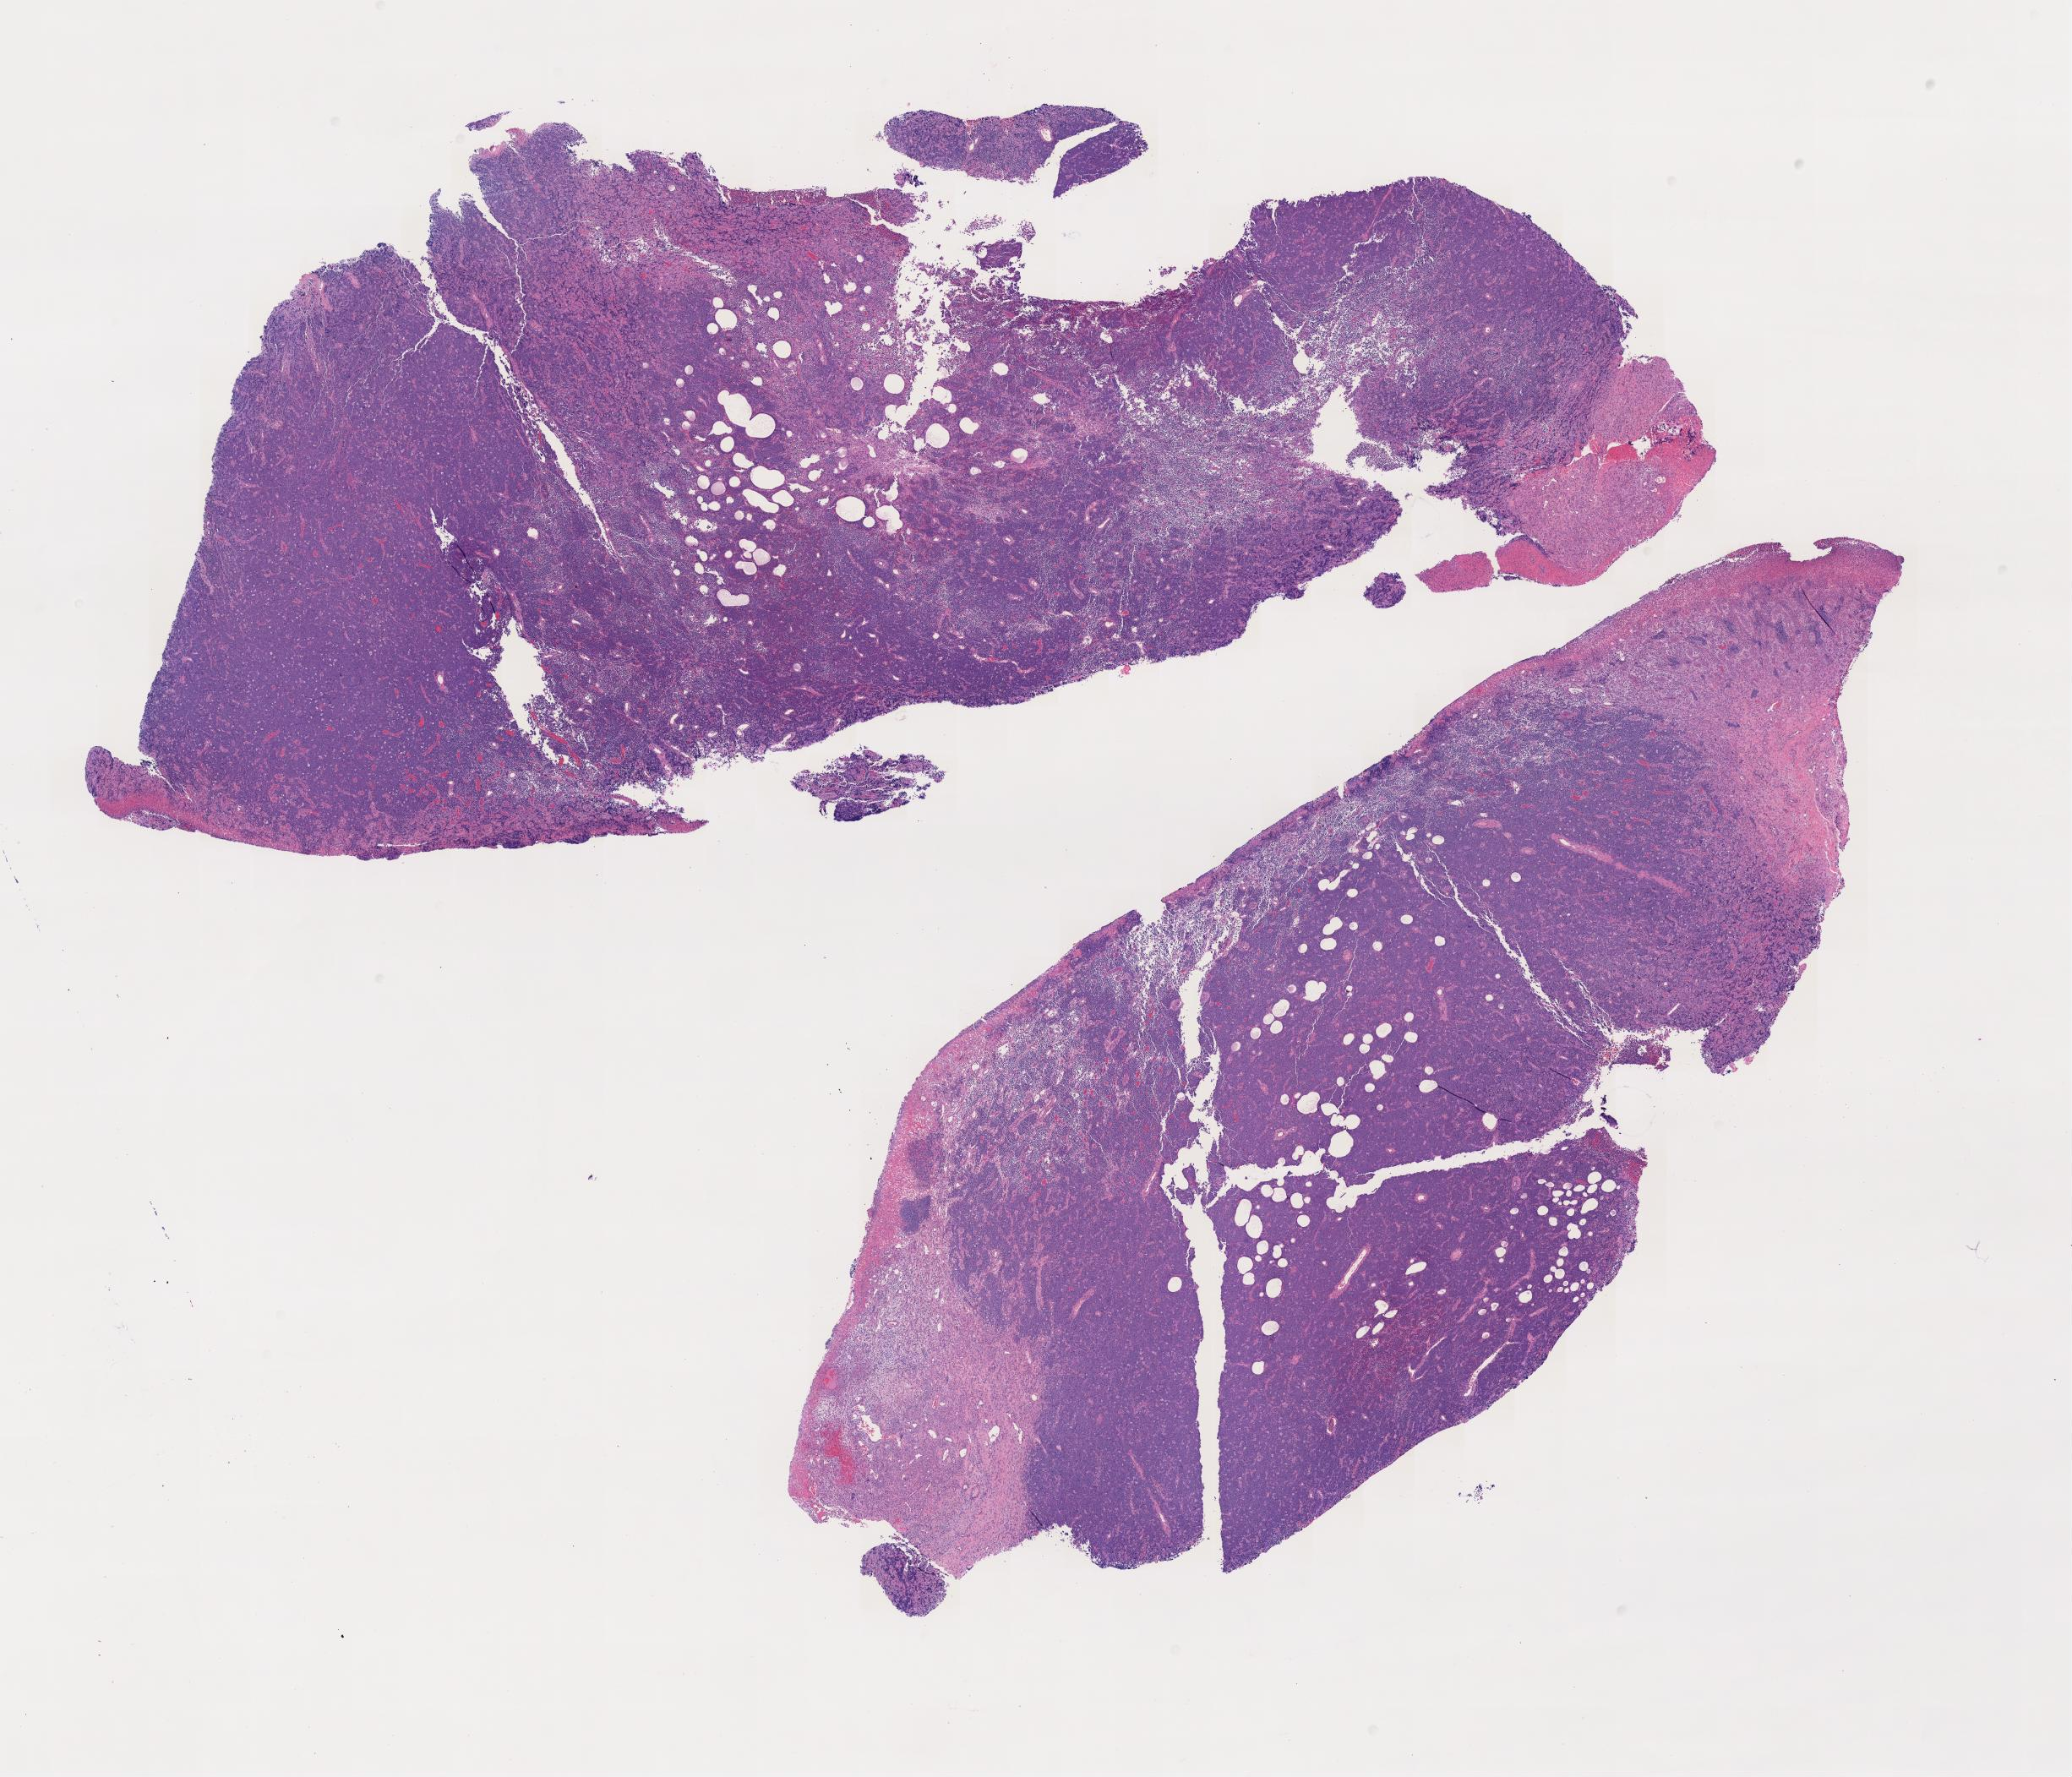
Hematoxylin and eosin (H&E) whole-slide image, a low-resolution overview of the entire scanned area; tumor tissue; anatomic site: cranium. Female patient; age at initial diagnosis 6 years.
- histologic diagnosis: Burkitt lymphoma, NOS